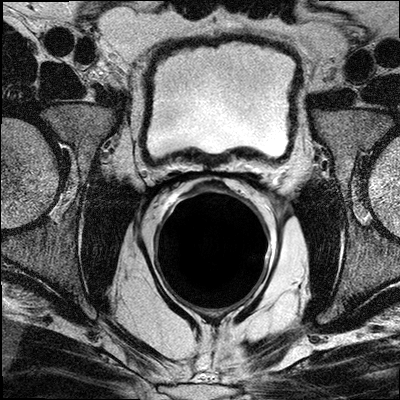
Pelvic MRI after prostatectomy (prostatic bed); 3 images, each a single mid-volume slice chosen by position (not for content).
Image 1: T2-weighted axial slice, slice 21 of 40, 3 mm slice thickness.
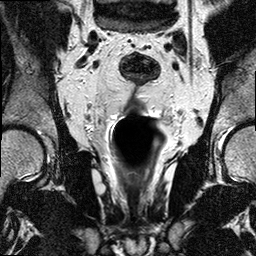
Image 2: T2-weighted coronal slice, series "T2W_TSE_COR", slice 15 of 28, 3 mm slice thickness.
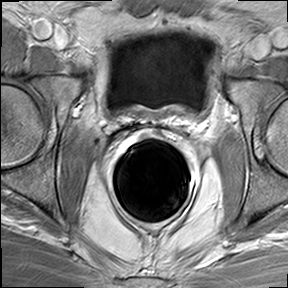
Image 3: DCE (dynamic gadolinium-enhanced) axial slice, series "dyn_THRIVE", slice 21 of 40, dynamic phase 5 of 9, 6 mm slice thickness.
Radiologist's MRI report for this examination:
FINDINGS: Regular findings seen within the surgical bed. Multiple surgical clips within the prostatic bed and around the anastomosis. Regular appearance of the anastomosis. No definite masses seen within the prostatic bed. No foci of suspicious enhancement in and around the prostatic bed. Unremarkable urinary bladder. No remnant seminal vesicles present. No suspiciously enlarged obturator and iliac lymph nodes. Several small lymph nodes seen along the iliac vessels bilateral and peri-rectal, non larger than 5 mm. The visualized osseous structures without evidence of involvement. IMPRESSION: No suspicious mass in the prostatic bed. No enlarged obturator or iliac lymph nodes. Normal appearance of the prostatic bed and anastomosis.

Prostatectomy specimen pathology (as recorded; the prostatectomy preceded this MRI, which images the post-surgical bed):
Specimen(s) Received A: RIGHT VAS DEFERENS B: PROSTATE AND SEMINAL VESICLES A. RIGHT VAS DEFERENS: SEGMENT OF VAS DEFERENS. NO TUMOR IDENTIFIED. B. PROSTATE AND SEMINAL VESICLES: PROSTATIC ADENOCARCINOMA, CONVENTIONAL TYPE. GLEASON GRADE 3+4 SCORE = 7/10. THE TUMOR IS CONFINED TO THE PROSTATE GLAND AND IS BILATERAL WITH PRIMARY INVOLVEMENT OF THE RIGHT LOBE. THE TUMOR OCCUPIES 10% OF THE TOTAL GLAND. EXTRAPROSTATIC EXTENSION NOT NOTED. INVASION OF SEMINAL VESICLES IS NOT IDENTIFIED. PERINEURAL INVASION IS PRESENT. LYMPHOVASCULAR SPACE IS ABSENT. THE SURGICAL MARGINS ARE NEGATIVE. LYMPH NODE SAMPLING: NO LYMPH NODES PRESENT. TREATMENT EFFECT ON CARCINOMA: NOT IDENTIFIED ADDITIONAL PATHOLOGIC FINDINGS: HIGH-GRADE PROSTATIC INTRAEPITHELIAL NEOPLASIA, ACUTE AND CHRONIC INFLAMMATION. COMMENT: AJCC PATHOLOGIC STAGING (pT2c, pNx, pMx. Gross Description The specimens are received fresh in two containers labeled with the patient' s name, hospital number and A. "Right Vas Deferens" and B. "Prostate and Seminal Vesicle".
Specimen A consists of a partial segment of the vas deferens measuring 4x0.5 cm. The tip is inked black and the margin is submitted in a single cassette labeled A.
Specimen B consists of a total prostatectomy specimen weighing 51.7 grams and measuring 4.4x4x3.3 cm. The right seminal vesicle measures 4.5x1.5x0.5 cm. The left seminal vesicle measures 4.7x0.7x0.5 cm. The right vas deferens appears incomplete and measures 2.7x0.6 cm. The left vas deferens measures 5.7x0.6 cm. The right surface of the prostate is inked black and the left surface is inked blue. The right and the left lobes appear symmetrical with slight nodularity of both lobes. The specimen is serially sectioned to reveal an irregular yellowish lesion in the right posterior lobe measuring 0.9x0.4 cm. There are no other lesions identified. The specimen is submitted in toto in cassettes as follows: B1 left vas deferens, B2 right apical margin, B3 thru B8 right anterior lobe sectioned from apex to base, B8 right bladder neck margin, B9 thru B17 right posterior lobe sectioned from apex to base with cassette B17 containing the seminal vesicle and B15 and B16 containing the lesion, B18 left apical margin, B19 thru B23 left anterior lobe sectioned from apex to base, B24 left bladder neck margin, B25 thru B32 left posterior lobe sectioned from apex to base with cassette B32 containing the seminal vesicle. Final Diagnosis A.RIGHT VAS DEFERENS: SEGMENT OF VAS DEFERENS. NO TUMOR IDENTIFIED.
B.PROSTATE AND SEMINAL VESICLES: PROSTATIC ADENOCARCINOMA, CONVENTIONAL TYPE. GLEASON GRADE 3+4 SCORE = 7/10. THE TUMOR IS CONFINED TO THE PROSTATE GLAND AND IS BILATERAL WITH PRIMARY INVOLVEMENT OF THE RIGHT LOBE. THE TUMOR OCCUPIES 10% OF THE TOTAL GLAND. EXTRAPROSTATIC EXTENSION NOT NOTED. INVASION OF SEMINAL VESICLES IS NOT IDENTIFIED. PERINEURAL INVASION IS PRESENT. LYMPHOVASCULAR SPACE IS ABSENT. THE SURGICAL MARGINS ARE NEGATIVE. LYMPH NODE SAMPLING: NO LYMPH NODES PRESENT.
TREATMENT EFFECT ON CARCINOMA: NOT IDENTIFIED ADDITIONAL PATHOLOGIC FINDINGS: HIGH-GRADE PROSTATIC INTRAEPITHELIAL NEOPLASIA, ACUTE AND CHRONIC INFLAMMATION.
COMMENT:AJCC PATHOLOGIC STAGING (pT2c, pNx, pMx).